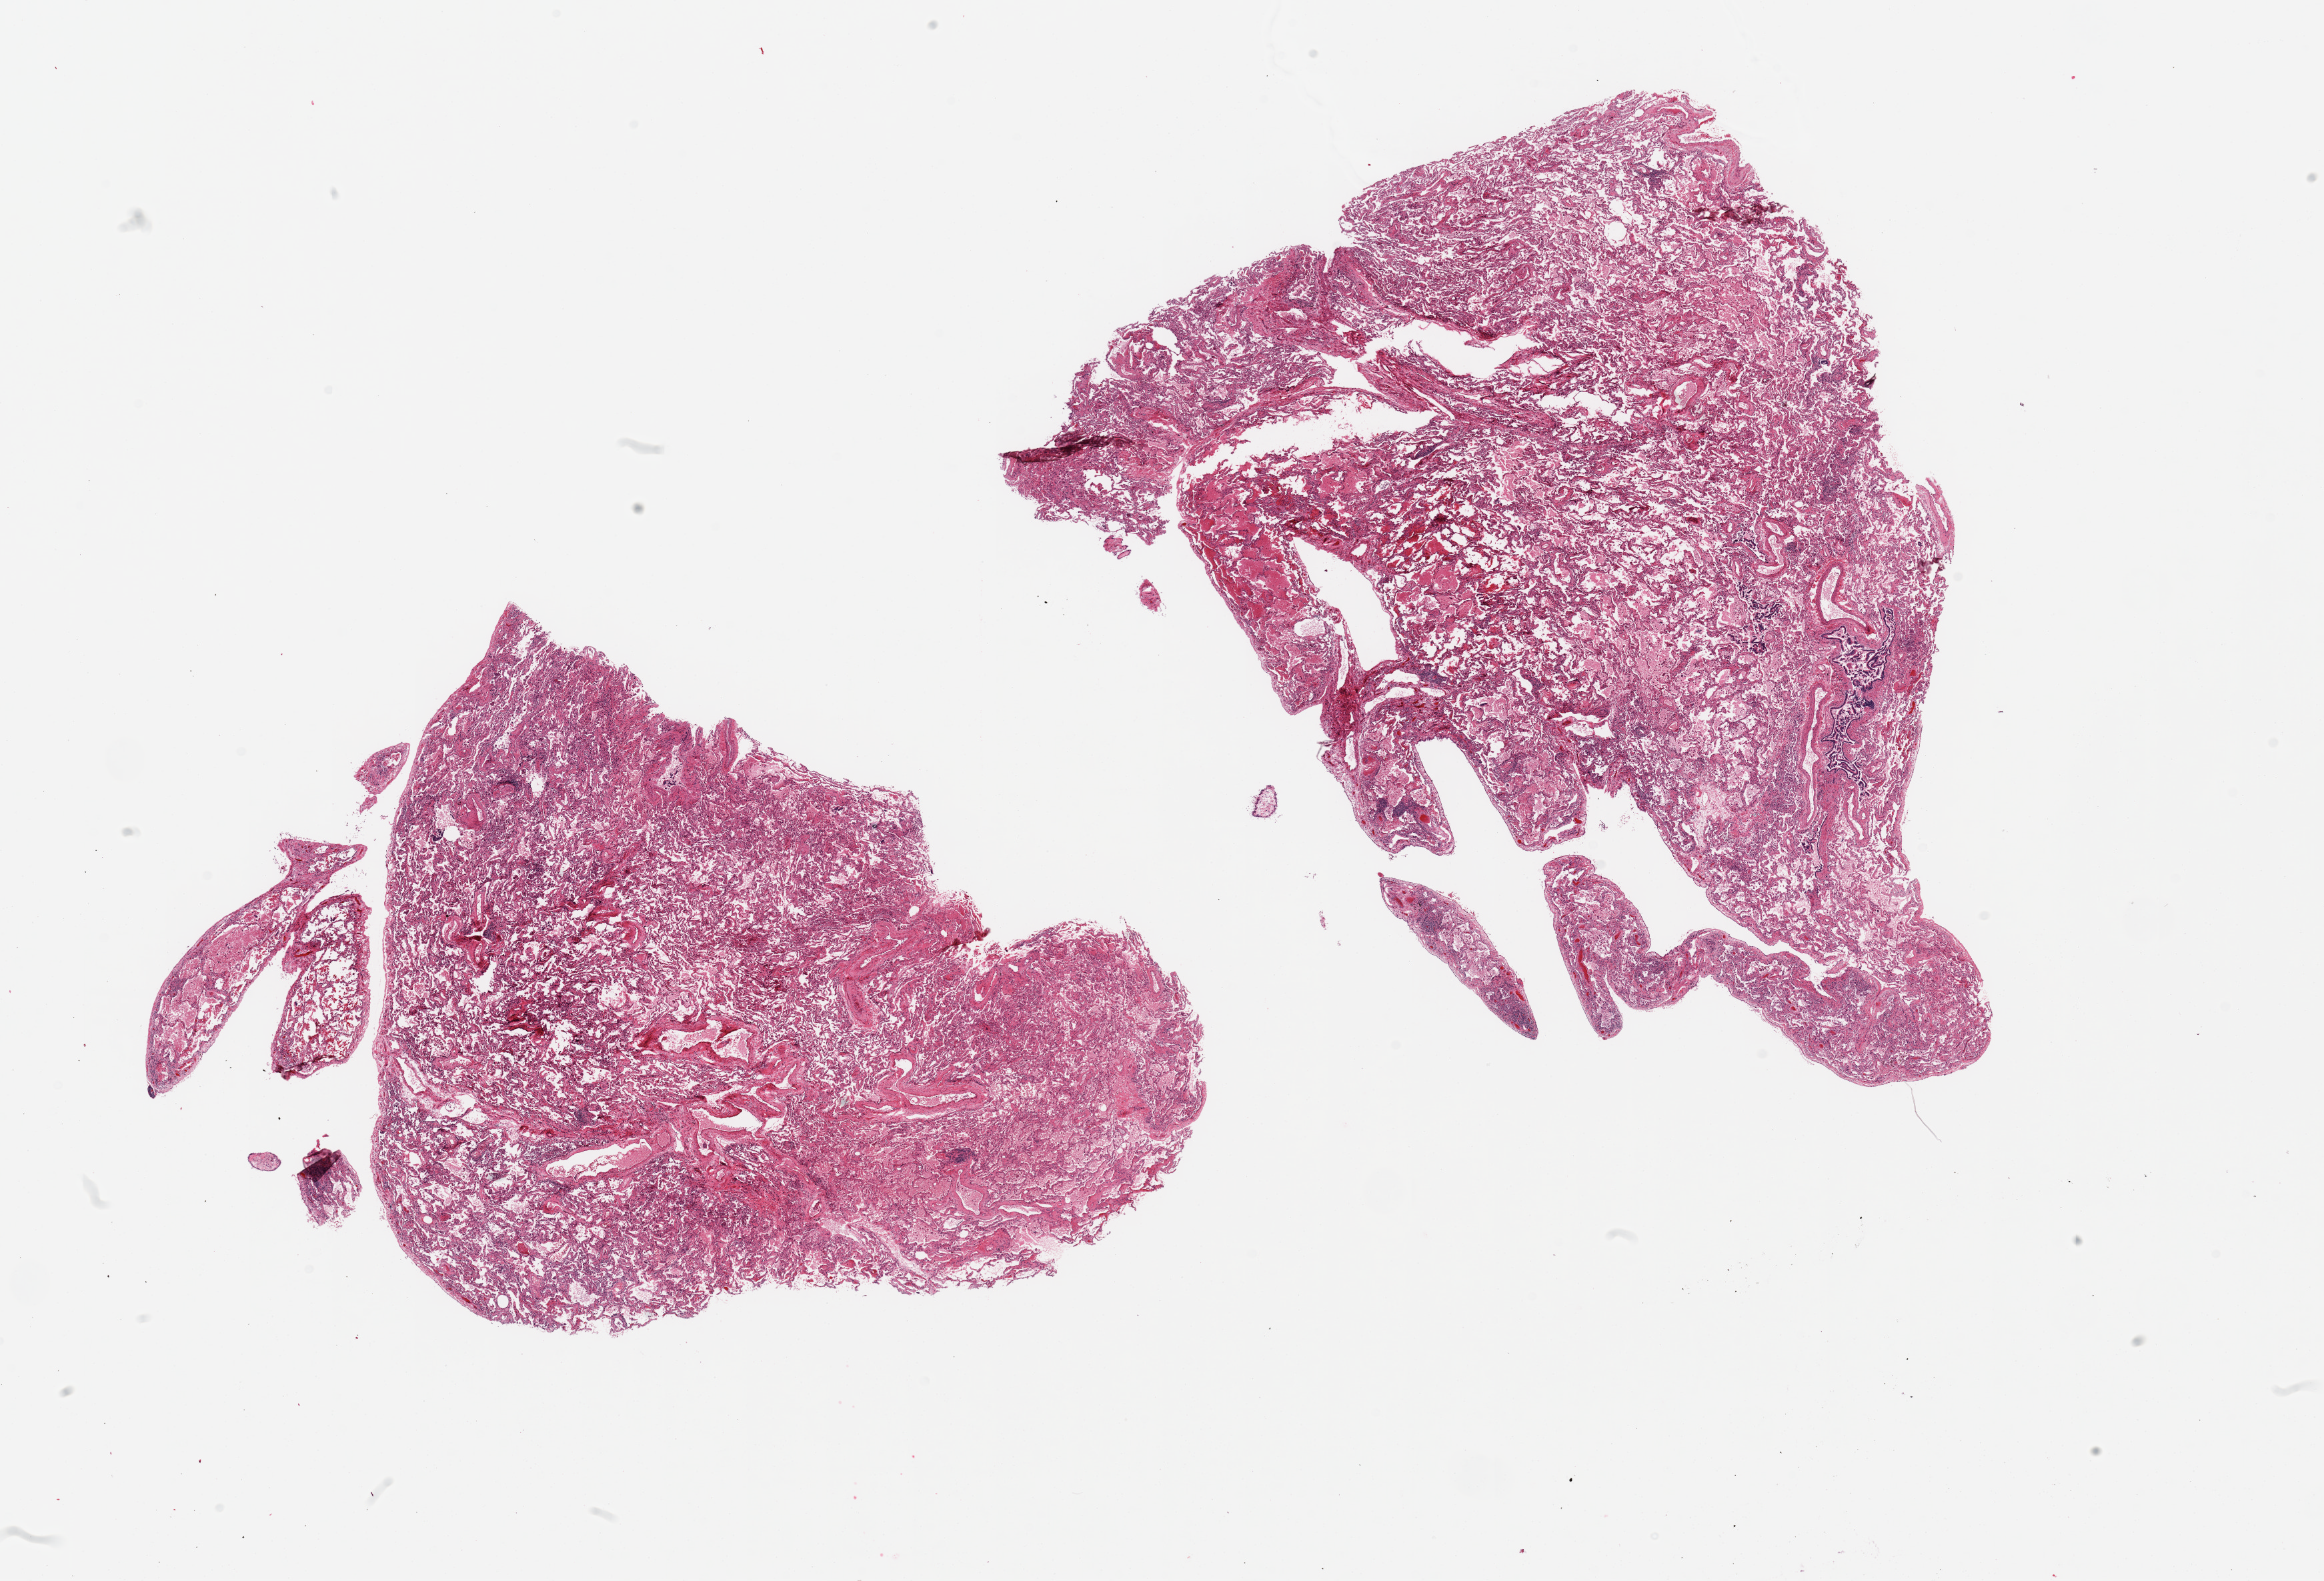
Whole-slide image, haematoxylin and eosin stain, a low-resolution overview of the entire scanned area, about 27.6 x 18.8 mm. PAXgene-fixed paraffin-embedded (PFPE) section. Target tissue: lung. Donor tissue sample. Donor: female.
- reviewer comment on this tissue sample: 2 pieces; many alveolar macrophages; perivascular fibrosis